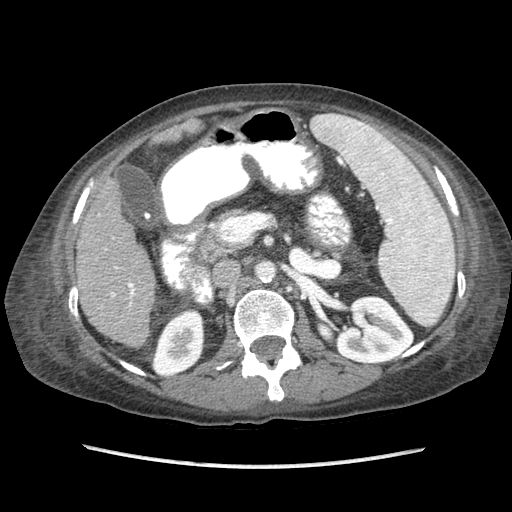
Contrast-enhanced abdominal CT (liver protocol), one axial slice. Position 33 of 87 along the scan axis. 120 kVp. Soft-tissue window (W 400 / L 40 HU). 512 × 512 image matrix. From the clinical record (not read from this slice): diagnosis: hepatocellular carcinoma (patient treated with transarterial chemoembolisation; whether this scan precedes or follows treatment is not stated here); TNM stage (as recorded): Stage-IIIB; Child-Pugh class: A; tumour differentiation: no biopsy; tumour nodularity: uninodular.
Annotated regions visible in this slice (semi-automatically segmented with operator editing):
- liver parenchyma outside the tumour (the mass and vessels are separate outlines, so this box may not span the whole liver): bounding box (x1, y1, x2, y2) in pixels: (76, 178, 156, 348)
- liver vessels: (105, 249, 135, 306)